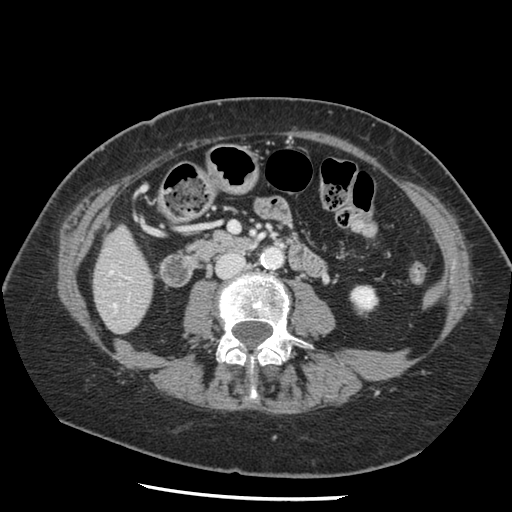
Contrast-enhanced abdominal CT, one axial slice. Position 31 of 148 along the scan axis. 120 kVp. Intravenous contrast given. Soft-tissue window (W 400 / L 40 HU). 2.5 mm slice thickness. 512 × 512 image matrix, field of view 330 × 330 mm. Female patient, age 85 years. Case-level facts recorded for this patient, not image findings: diagnosis: colorectal cancer liver metastases, imaged before liver resection; multiple liver metastases: no; largest metastasis: 0.9 cm.
Outlined on this slice (manually delineated by an expert):
- hepatic veins: bounding box (x1, y1, x2, y2) in pixels: (110, 272, 115, 306)
- liver: (94, 228, 153, 333)
- planned liver remnant (the part of the liver to remain after resection): (94, 228, 153, 332)